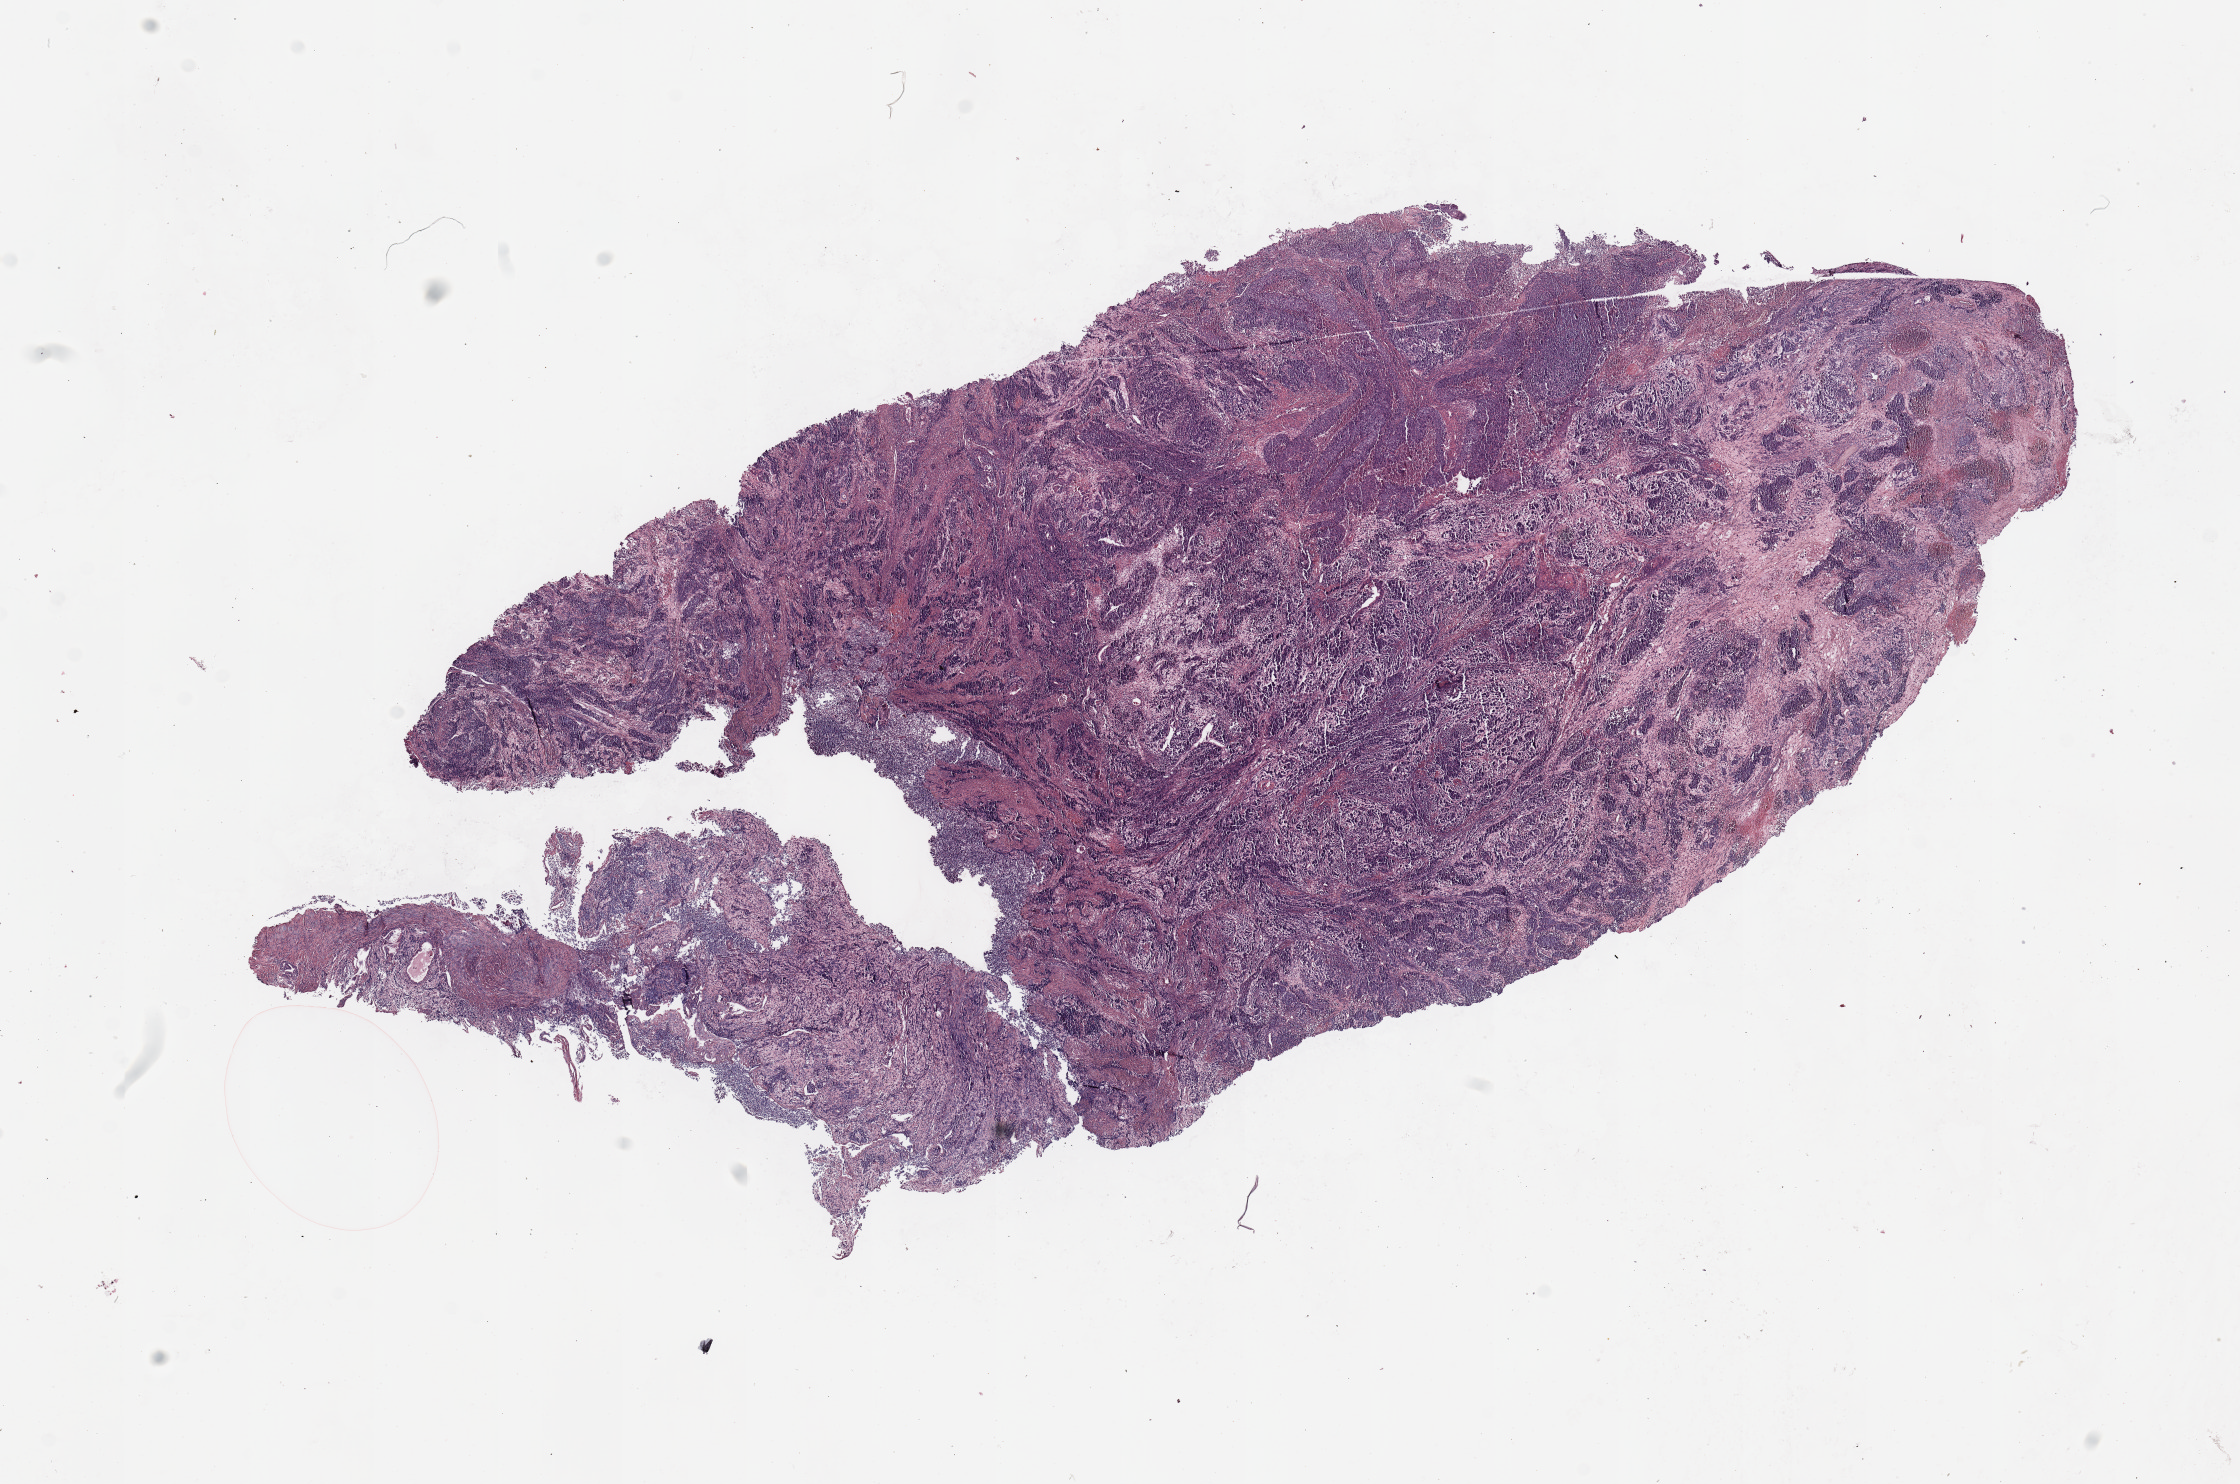
Digitized H&E-stained tissue section (whole slide), a low-resolution overview of the entire scanned area, about 17.7 x 11.7 mm (acquisition: 20x scan). Tumour tissue sample, uterus. 68-year-old female patient. Histologic grade: G3 (poorly differentiated).
Histologic diagnosis: Endometrioid adenocarcinoma, NOS. AJCC pathologic stage: I.